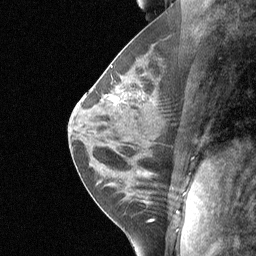
Breast MRI (dynamic contrast-enhanced), one sagittal slice. Position 30 of 64 along the scan axis. Dynamic contrast-enhanced study with each time point stored as its own series, time point 2 of 3 at this slice position (early post-contrast, ordered by acquisition time). 1.5 T. TE 4.8 ms, TR 27 ms. 2 mm slice thickness. 256 × 256 image matrix, field of view 200 × 200 mm. Patient: female, 27 years. From the clinical record (not read from this slice): setting: breast cancer imaged before/during neoadjuvant chemotherapy; receptor status: HR-positive, HER2-negative.
Outlined on this slice (semi-automatic segmentation, software-assisted and operator-edited):
- analysis volume of interest (the breast-tissue region the enhancement analysis was run in; not a lesion): box from (x=89, y=45) to (x=161, y=149) px
- tumour enhancement mask (voxels above the 90 % enhancement threshold inside the analysis volume of interest): (x=115, y=97)–(x=118, y=99)